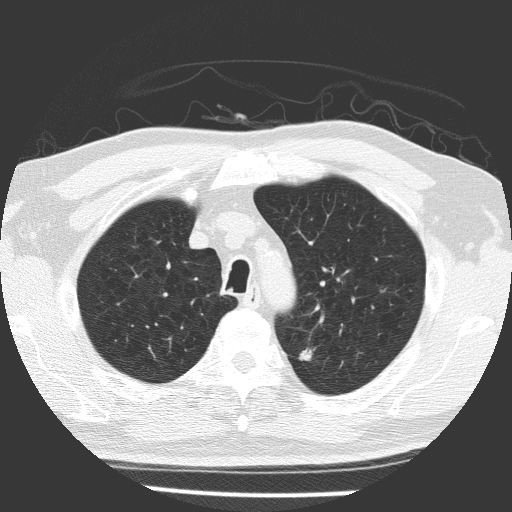
Low-dose screening chest CT, one axial slice; lung window (W 1500 / L -600 HU); 512 × 512 image matrix.
Annotated regions visible in this slice (expert manual segmentation):
- lesion 1 (tumor, upper lobe of left lung): bounding box [x1, y1, x2, y2] px = [299, 348, 315, 361]